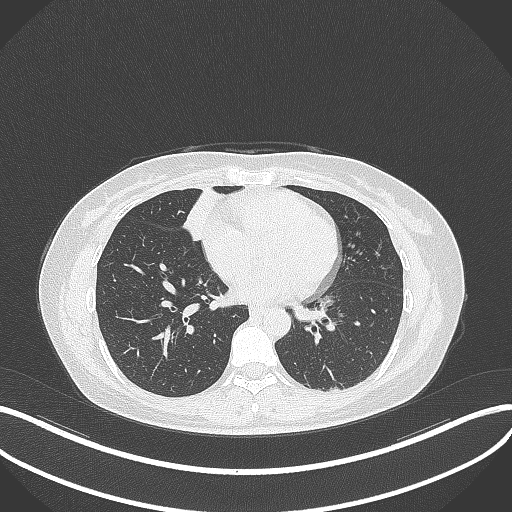
Chest CT, one axial slice; slice 112 of 284 in the series (ordered by position); reconstruction kernel B70f; lung window (W 1500 / L -600 HU); 512 × 512 image matrix, field of view 400 × 400 mm. Patient: female, 43 years. From the clinical record (not read from this slice): clinical TNM (as recorded): T1c N3 M1; histopathological grade: G1.
Structures marked on this image (bounding box drawn by a radiologist):
- lung tumour (recorded histology: adenocarcinoma): box from (x=183, y=182) to (x=226, y=246) px